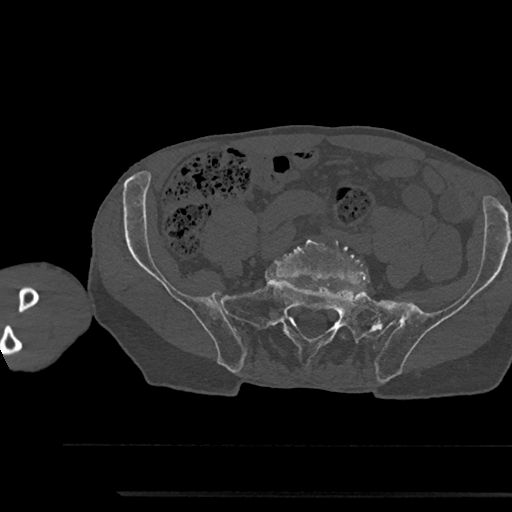
CT including the spine, one axial slice; position 308 of 797 along the scan axis; reconstruction kernel Br40s/3; bone window (W 1800 / L 400 HU); 0.5 mm slice thickness; 512 × 512 image matrix. Patient: male, 79 years. From the clinical record (not read from this slice): primary cancer: prostate.
Outlined on this slice (semi-automatically segmented with operator editing):
- L5 vertebra: box from (x=274, y=234) to (x=369, y=339) px